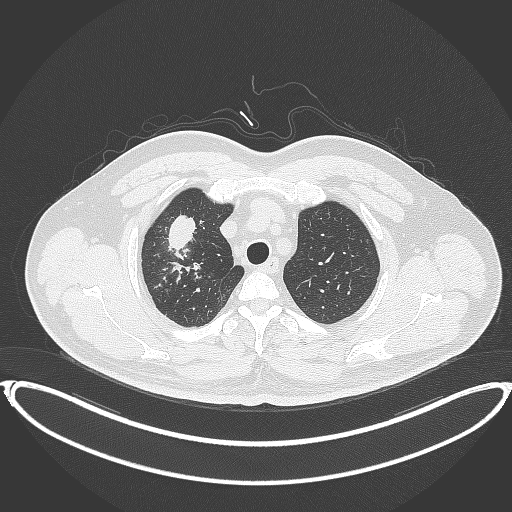
Chest CT, one axial slice; position 319 of 399 along the scan axis; lung window (W 1500 / L -600 HU); 1 mm slice thickness; 512 × 512 image matrix, field of view 445 × 445 mm. Male patient, age 53 years. From the clinical record (not read from this slice): clinical TNM (as recorded): T2a N0 M0.
Structures marked on this image (rectangle marked by the reading radiologist):
- lung tumour (recorded histology: adenocarcinoma): bounding box (x1, y1, x2, y2) in pixels: (166, 211, 202, 264)